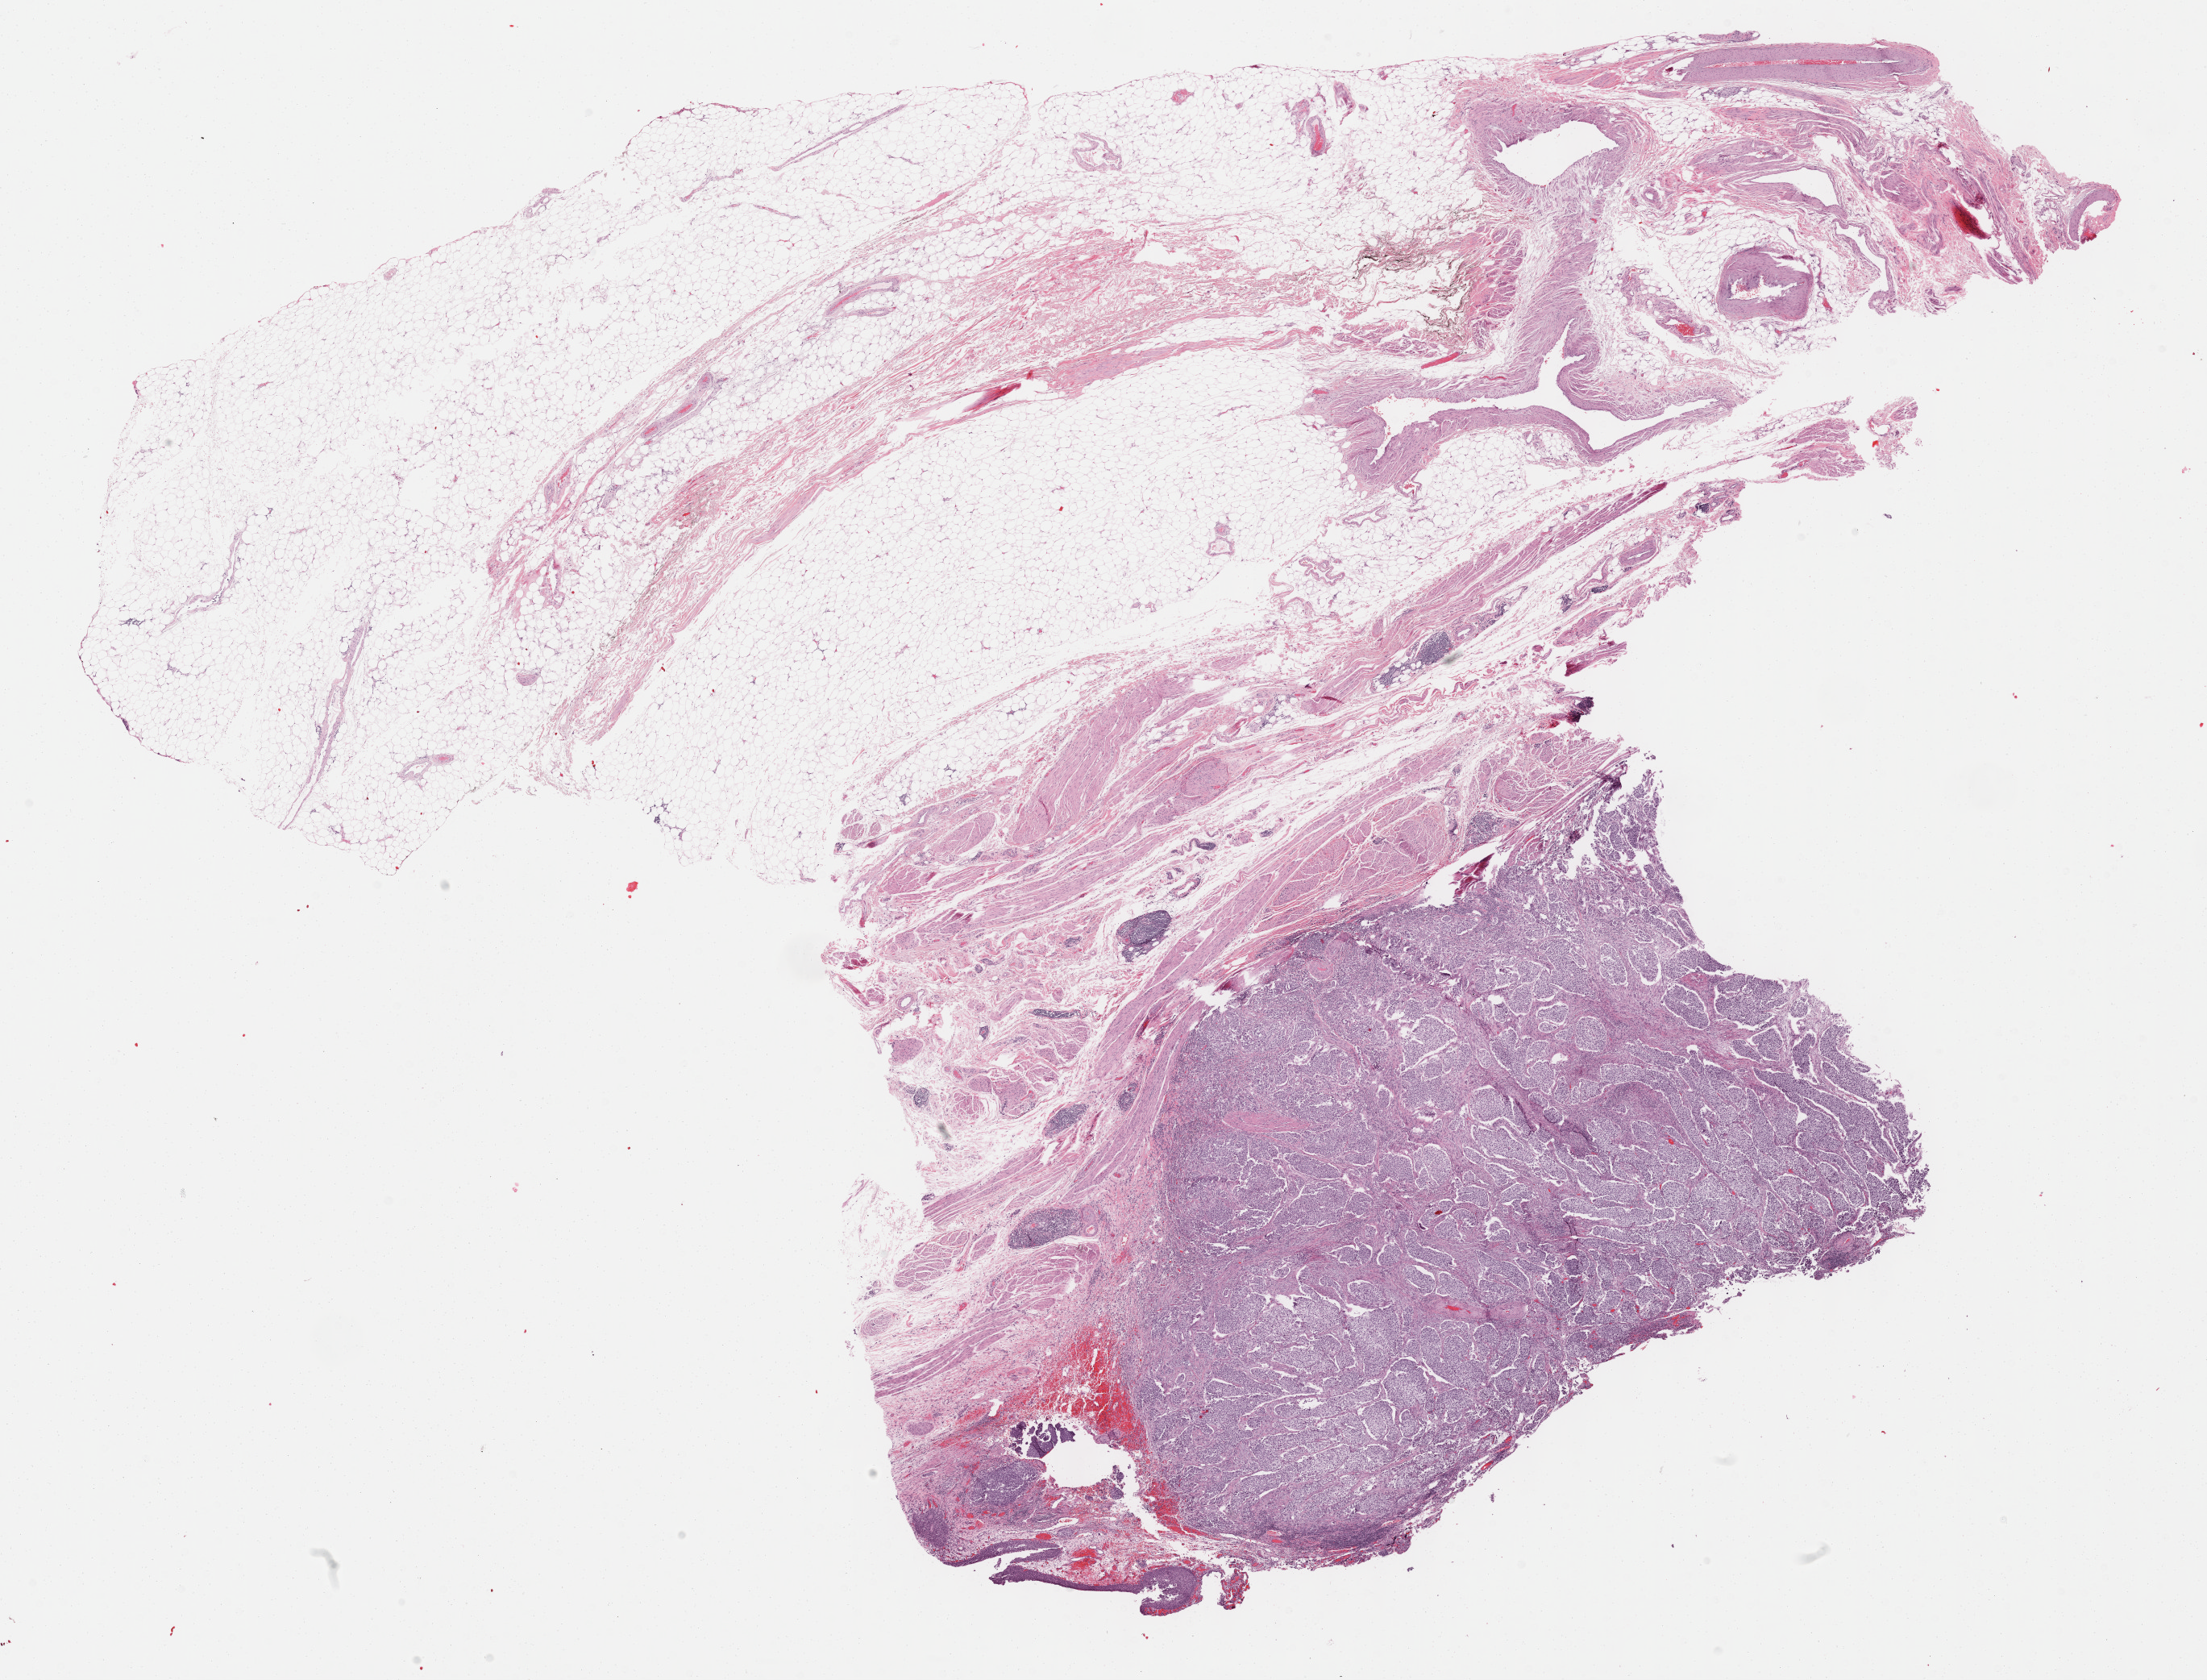
Digitized Hematoxylin and eosin (H&E) stained tissue section (whole slide) — low-resolution overview of the scanned area, about 22.1 x 16.9 mm (slide scanned at 40x). Formalin-fixed paraffin-embedded (FFPE) diagnostic section. Sample: primary tumour, bladder. Female, age 73 years at initial diagnosis.
Histologic diagnosis: Papillary transitional cell carcinoma.